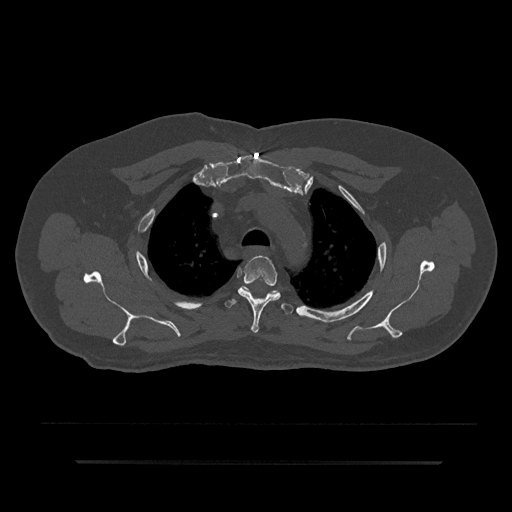
CT including the spine, one axial slice. Slice 650 of 797 in the series (ordered by position). 120 kVp. Bone window (W 1800 / L 400 HU). 0.5 mm slice thickness. 512 × 512 image matrix. Patient: male, 59 years. Case-level facts recorded for this patient, not image findings: primary cancer: bile ducts.
Annotated regions visible in this slice (semi-automatically segmented with operator editing):
- T3 vertebra: box from (x=238, y=255) to (x=281, y=333) px
- T4 vertebra: (x=224, y=292)–(x=294, y=315)